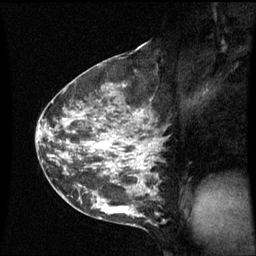
Breast MRI (dynamic contrast-enhanced), one sagittal slice. Slice 31 of 60 in the series (ordered by position). Dynamic contrast-enhanced series, image 2 of 3 at this slice position (ordered by acquisition). 1.5 T. TE 4.2 ms, TR 8.9 ms. 2.4 mm slice thickness. 256 × 256 image matrix, field of view 210 × 210 mm. Patient: female, 42 years. Case-level facts recorded for this patient, not image findings: setting: breast cancer imaged before/during neoadjuvant chemotherapy; receptor status: HER2-positive.
Structures marked on this image (semi-automatically segmented with operator editing):
- analysis volume of interest (the breast-tissue region the enhancement analysis was run in; not a lesion): bounding box [x1, y1, x2, y2] px = [62, 93, 161, 210]
- tumour enhancement mask (voxels above the 70 % enhancement threshold inside the analysis volume of interest): [67, 112, 154, 185]